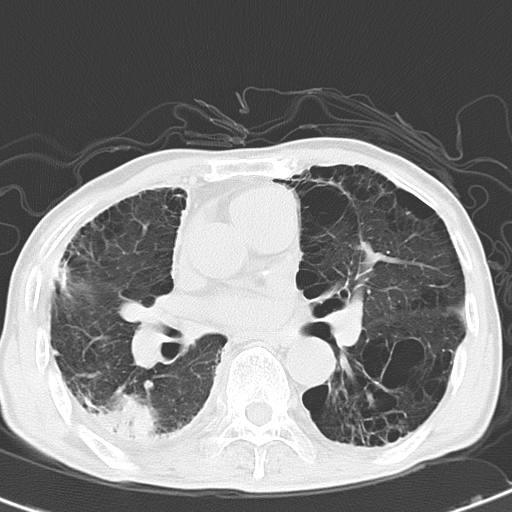
Chest CT, one axial slice. Position 25 of 51 along the scan axis. Reconstruction kernel B70f. Lung window (W 1500 / L -600 HU). 6 mm slice thickness. 512 × 512 image matrix, field of view 279 × 279 mm. Male patient, age 67 years. From the clinical record (not read from this slice): clinical TNM (as recorded): T2 N3 M1.
Outlined on this slice (bounding box drawn by a radiologist):
- lung tumour (recorded histology: adenocarcinoma): box from (x=101, y=393) to (x=157, y=449) px